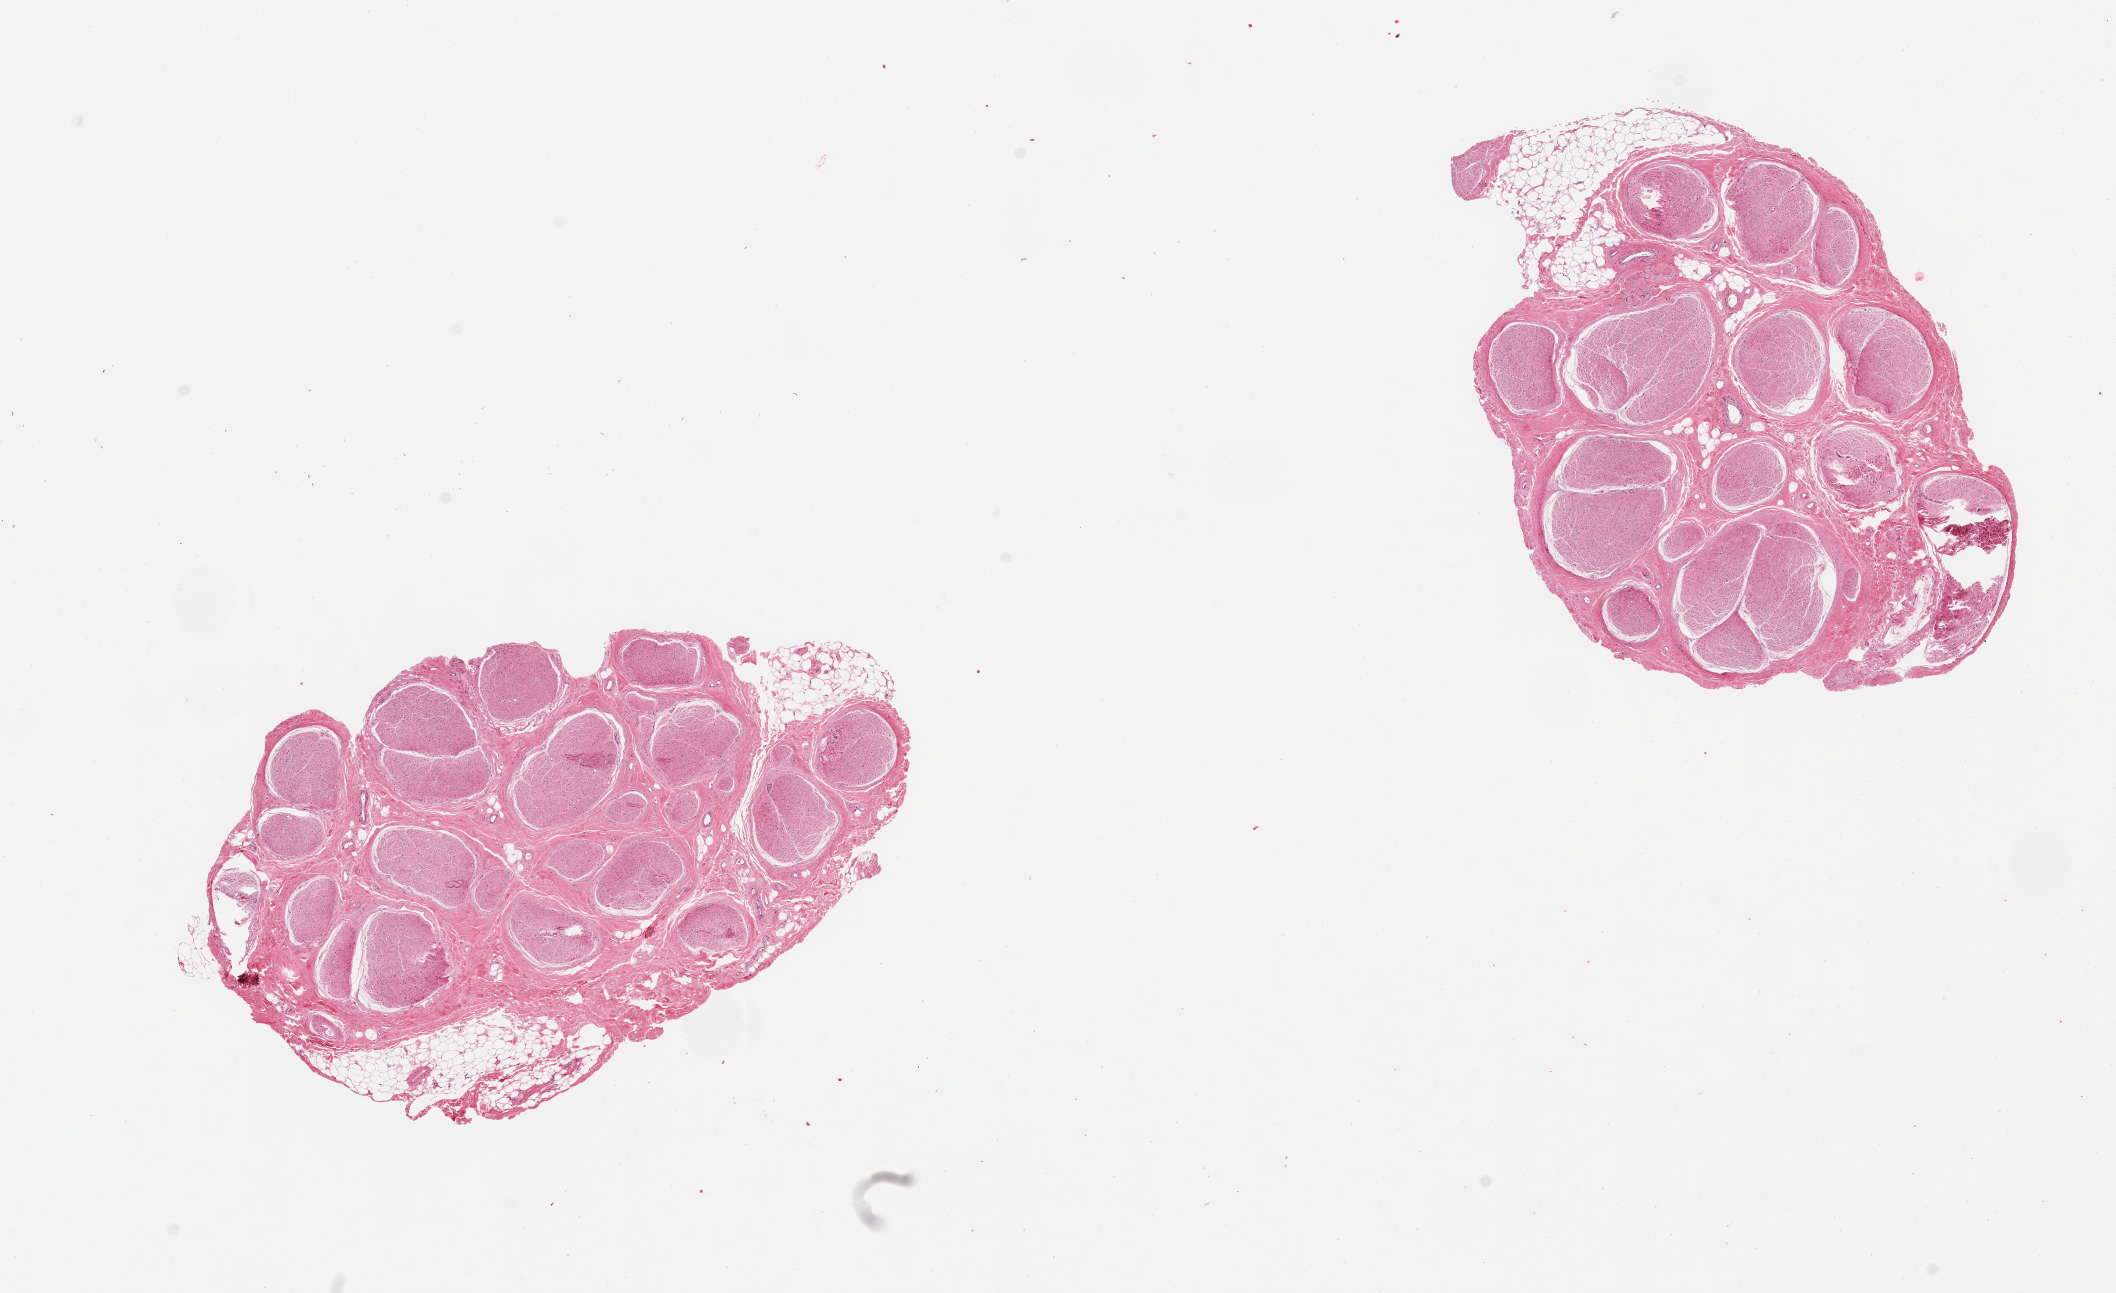
Digitized H&E-stained section — shown as a low-resolution overview of the whole scanned area (about 16.7 x 10.2 mm); PAXgene-fixed paraffin-embedded (PFPE) section; section of tibial nerve (target tissue); donor tissue sample. Donor sex: male.
Pathologist's review note for this sample: 2 pieces good clean sections; trace nubbins of fat, ~0.5mm.